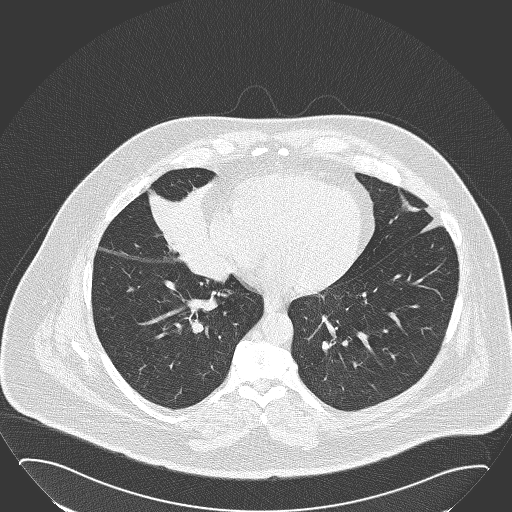
Low-dose screening chest CT, one axial slice. Slice 67 of 168 in the series (ordered by position). Reconstruction kernel B50f. 120 kVp. Lung window (W 1500 / L -600 HU). 2 mm slice thickness. 512 × 512 image matrix, field of view 432 × 432 mm.
Outlined on this slice (manually delineated by an expert):
- lesion 1 (tumor, hilum of right lung): bounding box <150,181,230,283> (left, top, right, bottom; pixels)